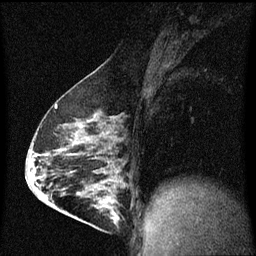
Breast MRI (dynamic contrast-enhanced), one sagittal slice; slice 34 of 60 in the series (ordered by position); dynamic contrast-enhanced series, image 2 of 3 at this slice position (ordered by acquisition); 1.5 T; TE 4.2 ms, TR 8 ms; 2 mm slice thickness; 256 × 256 image matrix. Female patient, age 63 years.
Structures marked on this image (semi-automatically segmented with operator editing):
- analysis volume of interest (the breast-tissue region the enhancement analysis was run in; not a lesion): box from (x=88, y=182) to (x=127, y=229) px
- tumour enhancement mask (voxels above the 70 % enhancement threshold inside the analysis volume of interest): (x=94, y=182)–(x=119, y=223)